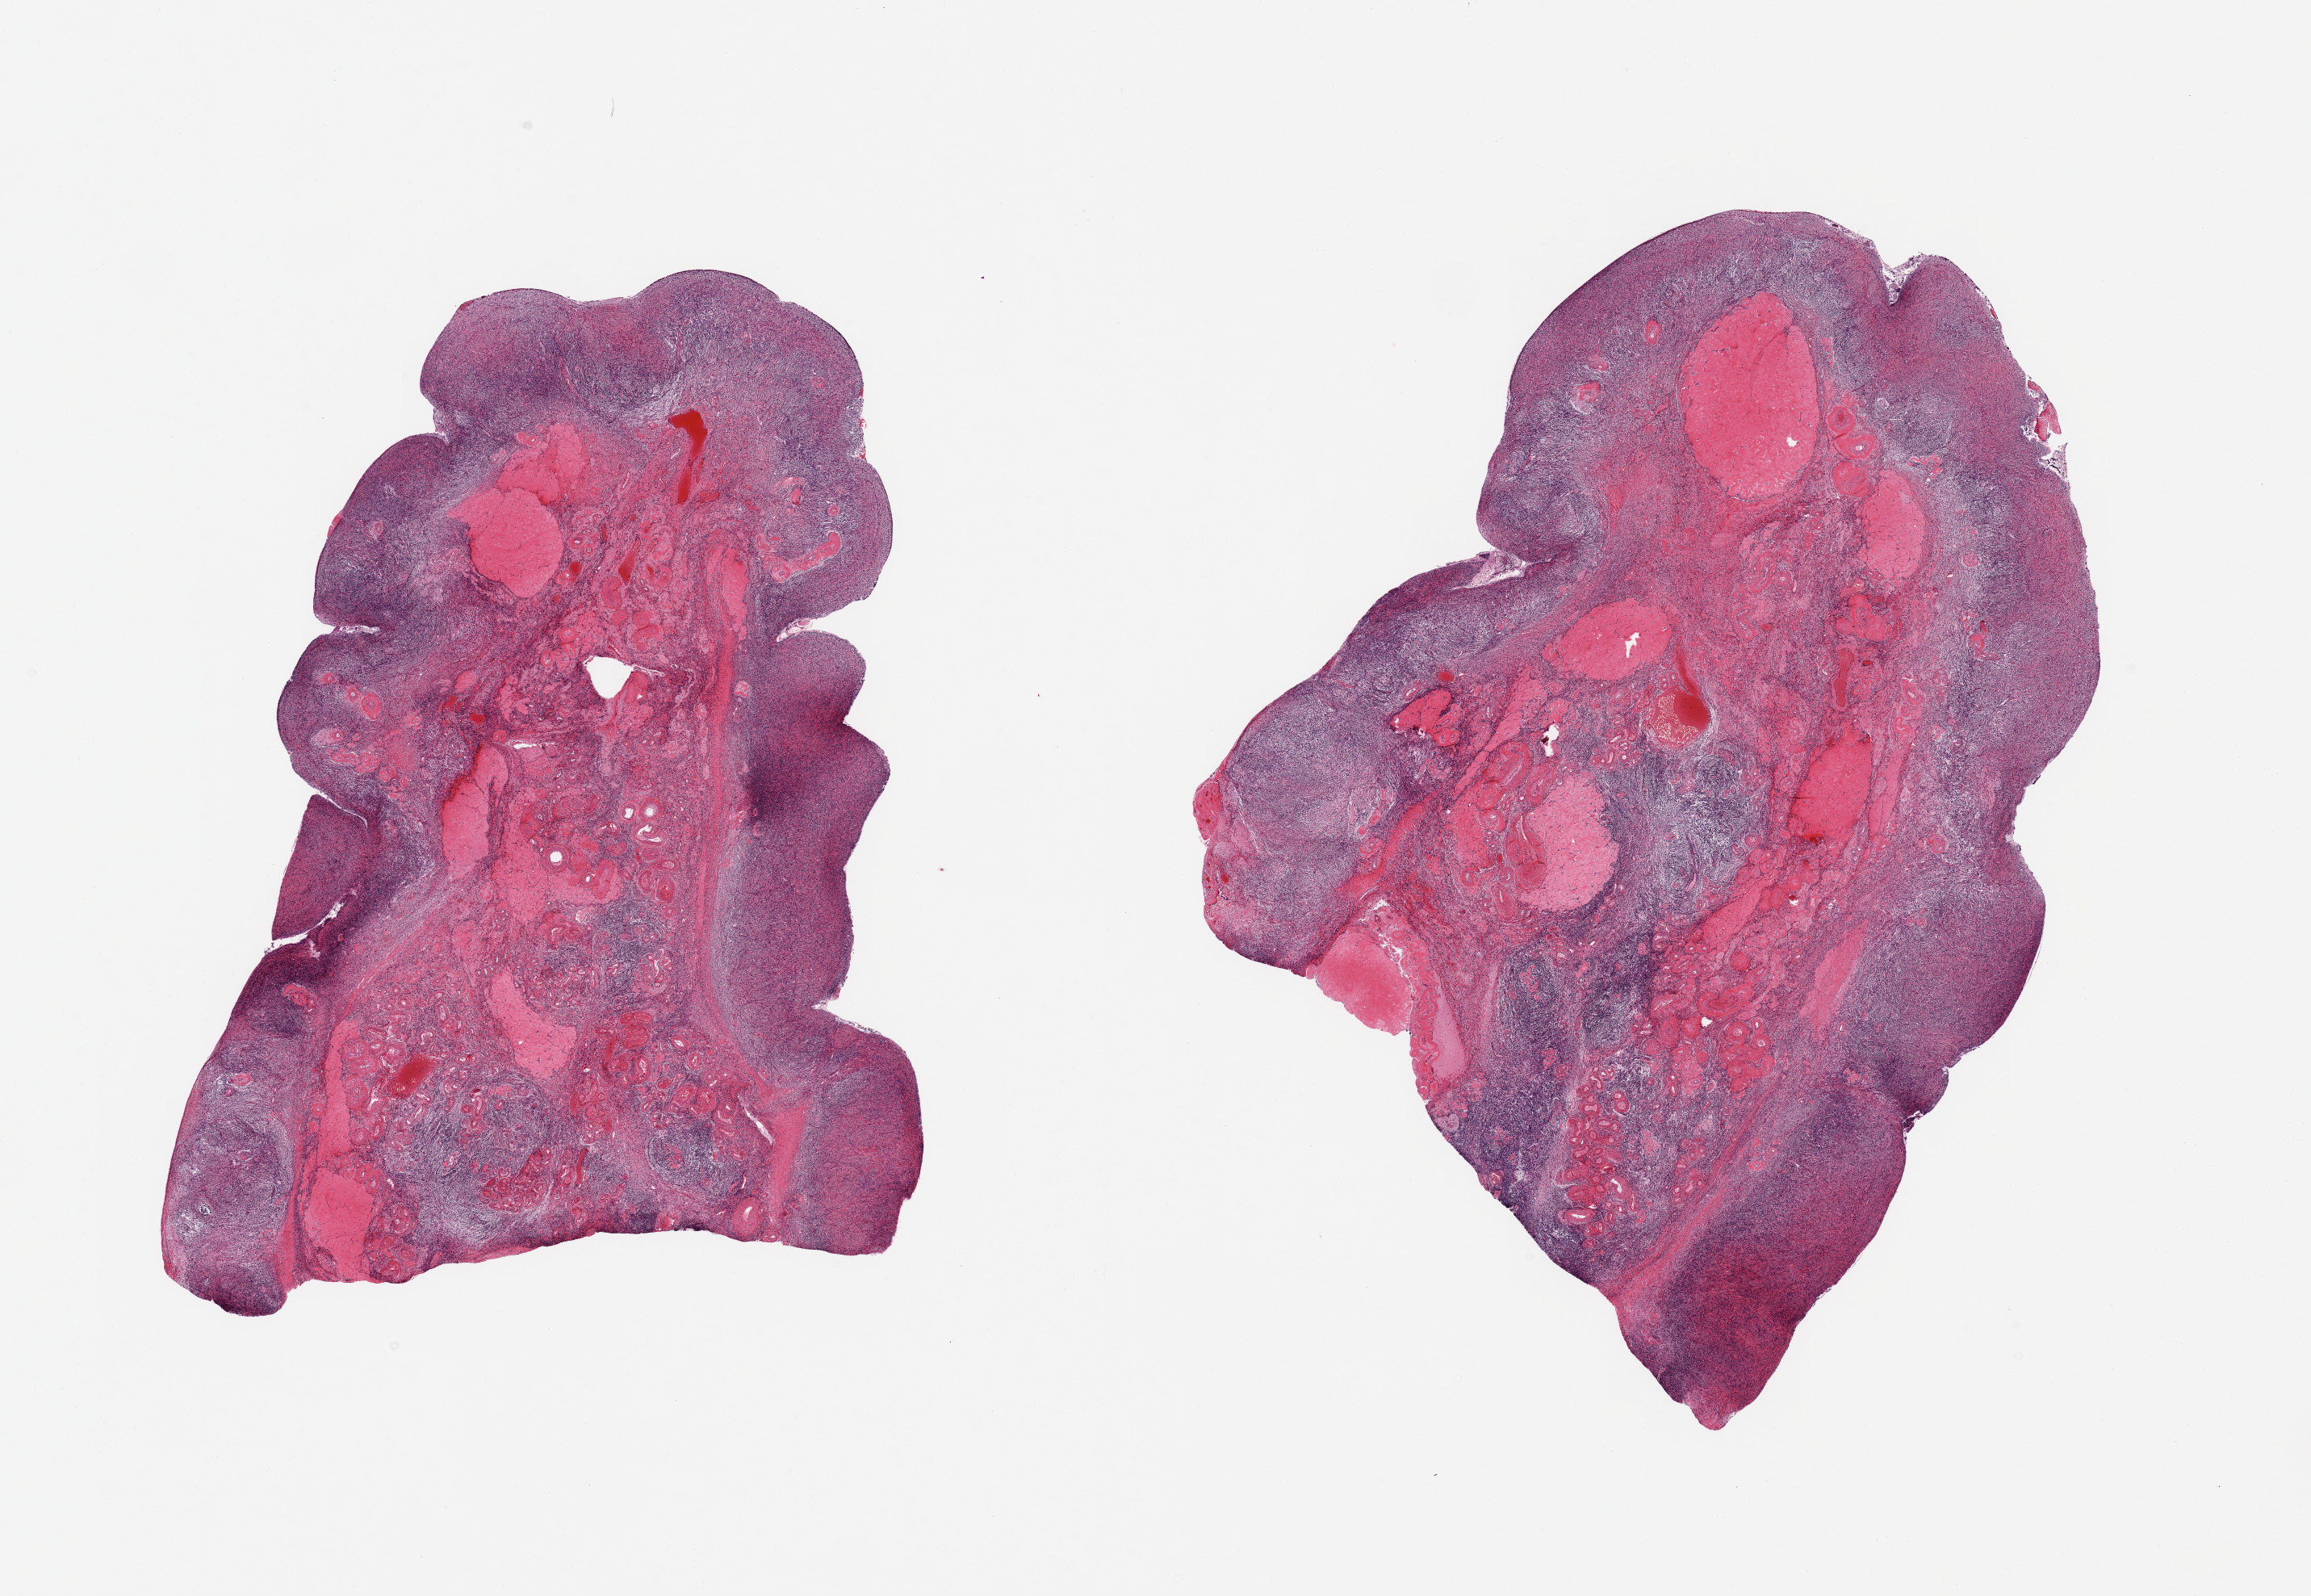
Digitized H&E-stained section, brightfield — a low-resolution overview of the entire scanned area, about 22.6 x 15.6 mm (from a 20x scan); PAXgene-fixed, paraffin-embedded tissue; target tissue: ovary; tissue donor sample. Donor sex: female.
Reviewer comment on this tissue sample: 2 pieces; corpora albicantia comprise 20%.